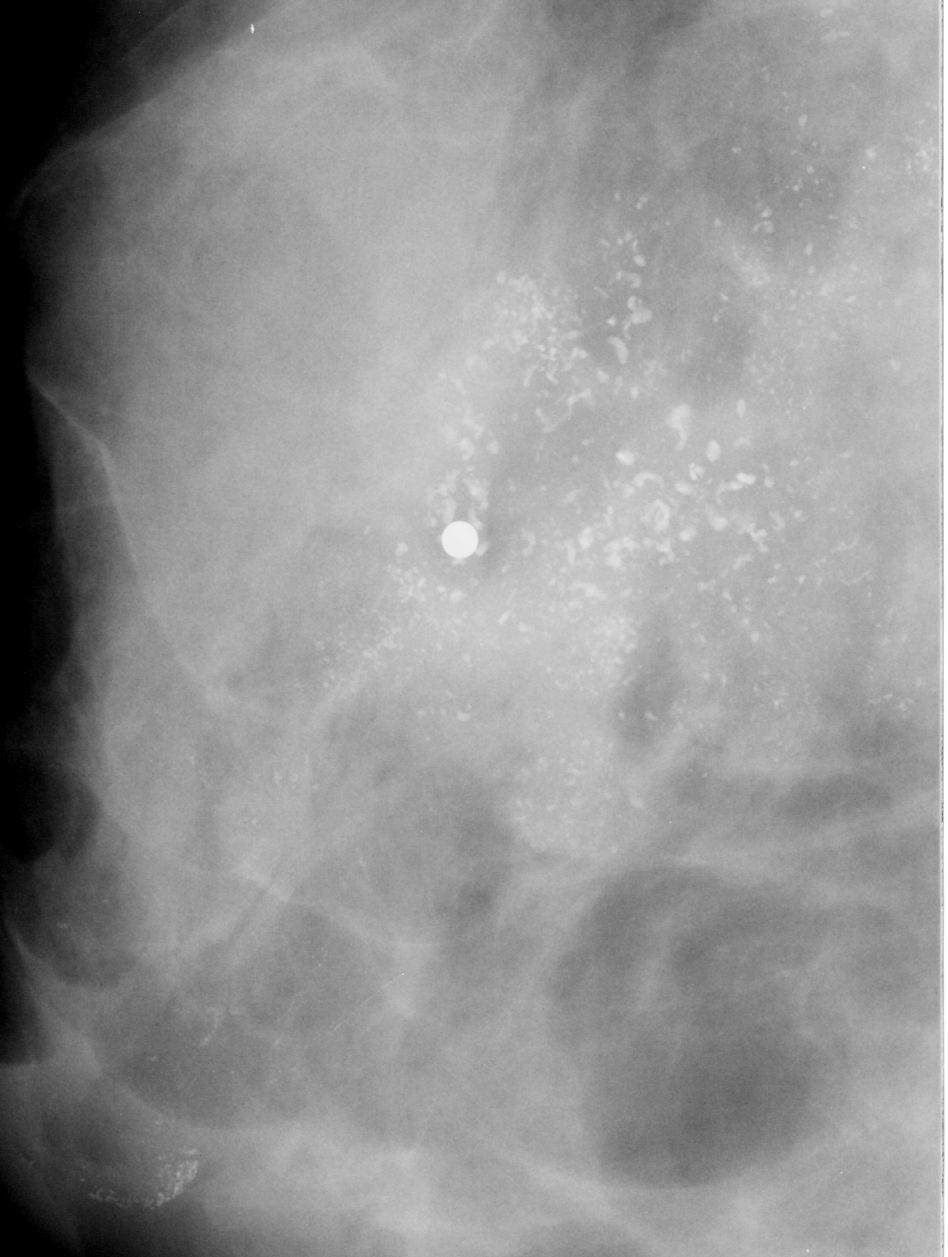
Cropped region of a digitized screen-film mammogram centred on a radiologist-marked abnormality; right breast; MLO view; BI-RADS breast density category 3 (scale 1–4).
Marked abnormality: calcifications, morphology pleomorphic, distribution regional; BI-RADS assessment category 5; pathology (as recorded): malignant.